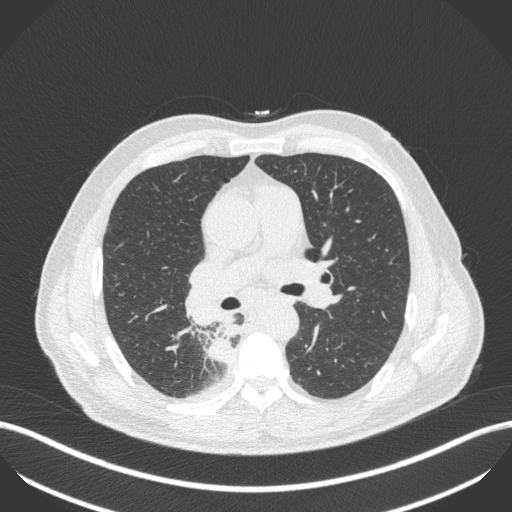
Chest CT, one axial slice. Slice 271 of 451 in the series (ordered by position). Reconstruction kernel B31f. Lung window (W 1500 / L -600 HU). 1 mm slice thickness. 512 × 512 image matrix. Patient: male, 61 years. Case-level facts recorded for this patient, not image findings: clinical TNM (as recorded): T1 N0 M0; histopathological grade: G3.
Structures marked on this image (bounding box drawn by a radiologist):
- lung tumour (recorded histology: small cell carcinoma): bounding box <208,335,234,365> (left, top, right, bottom; pixels)